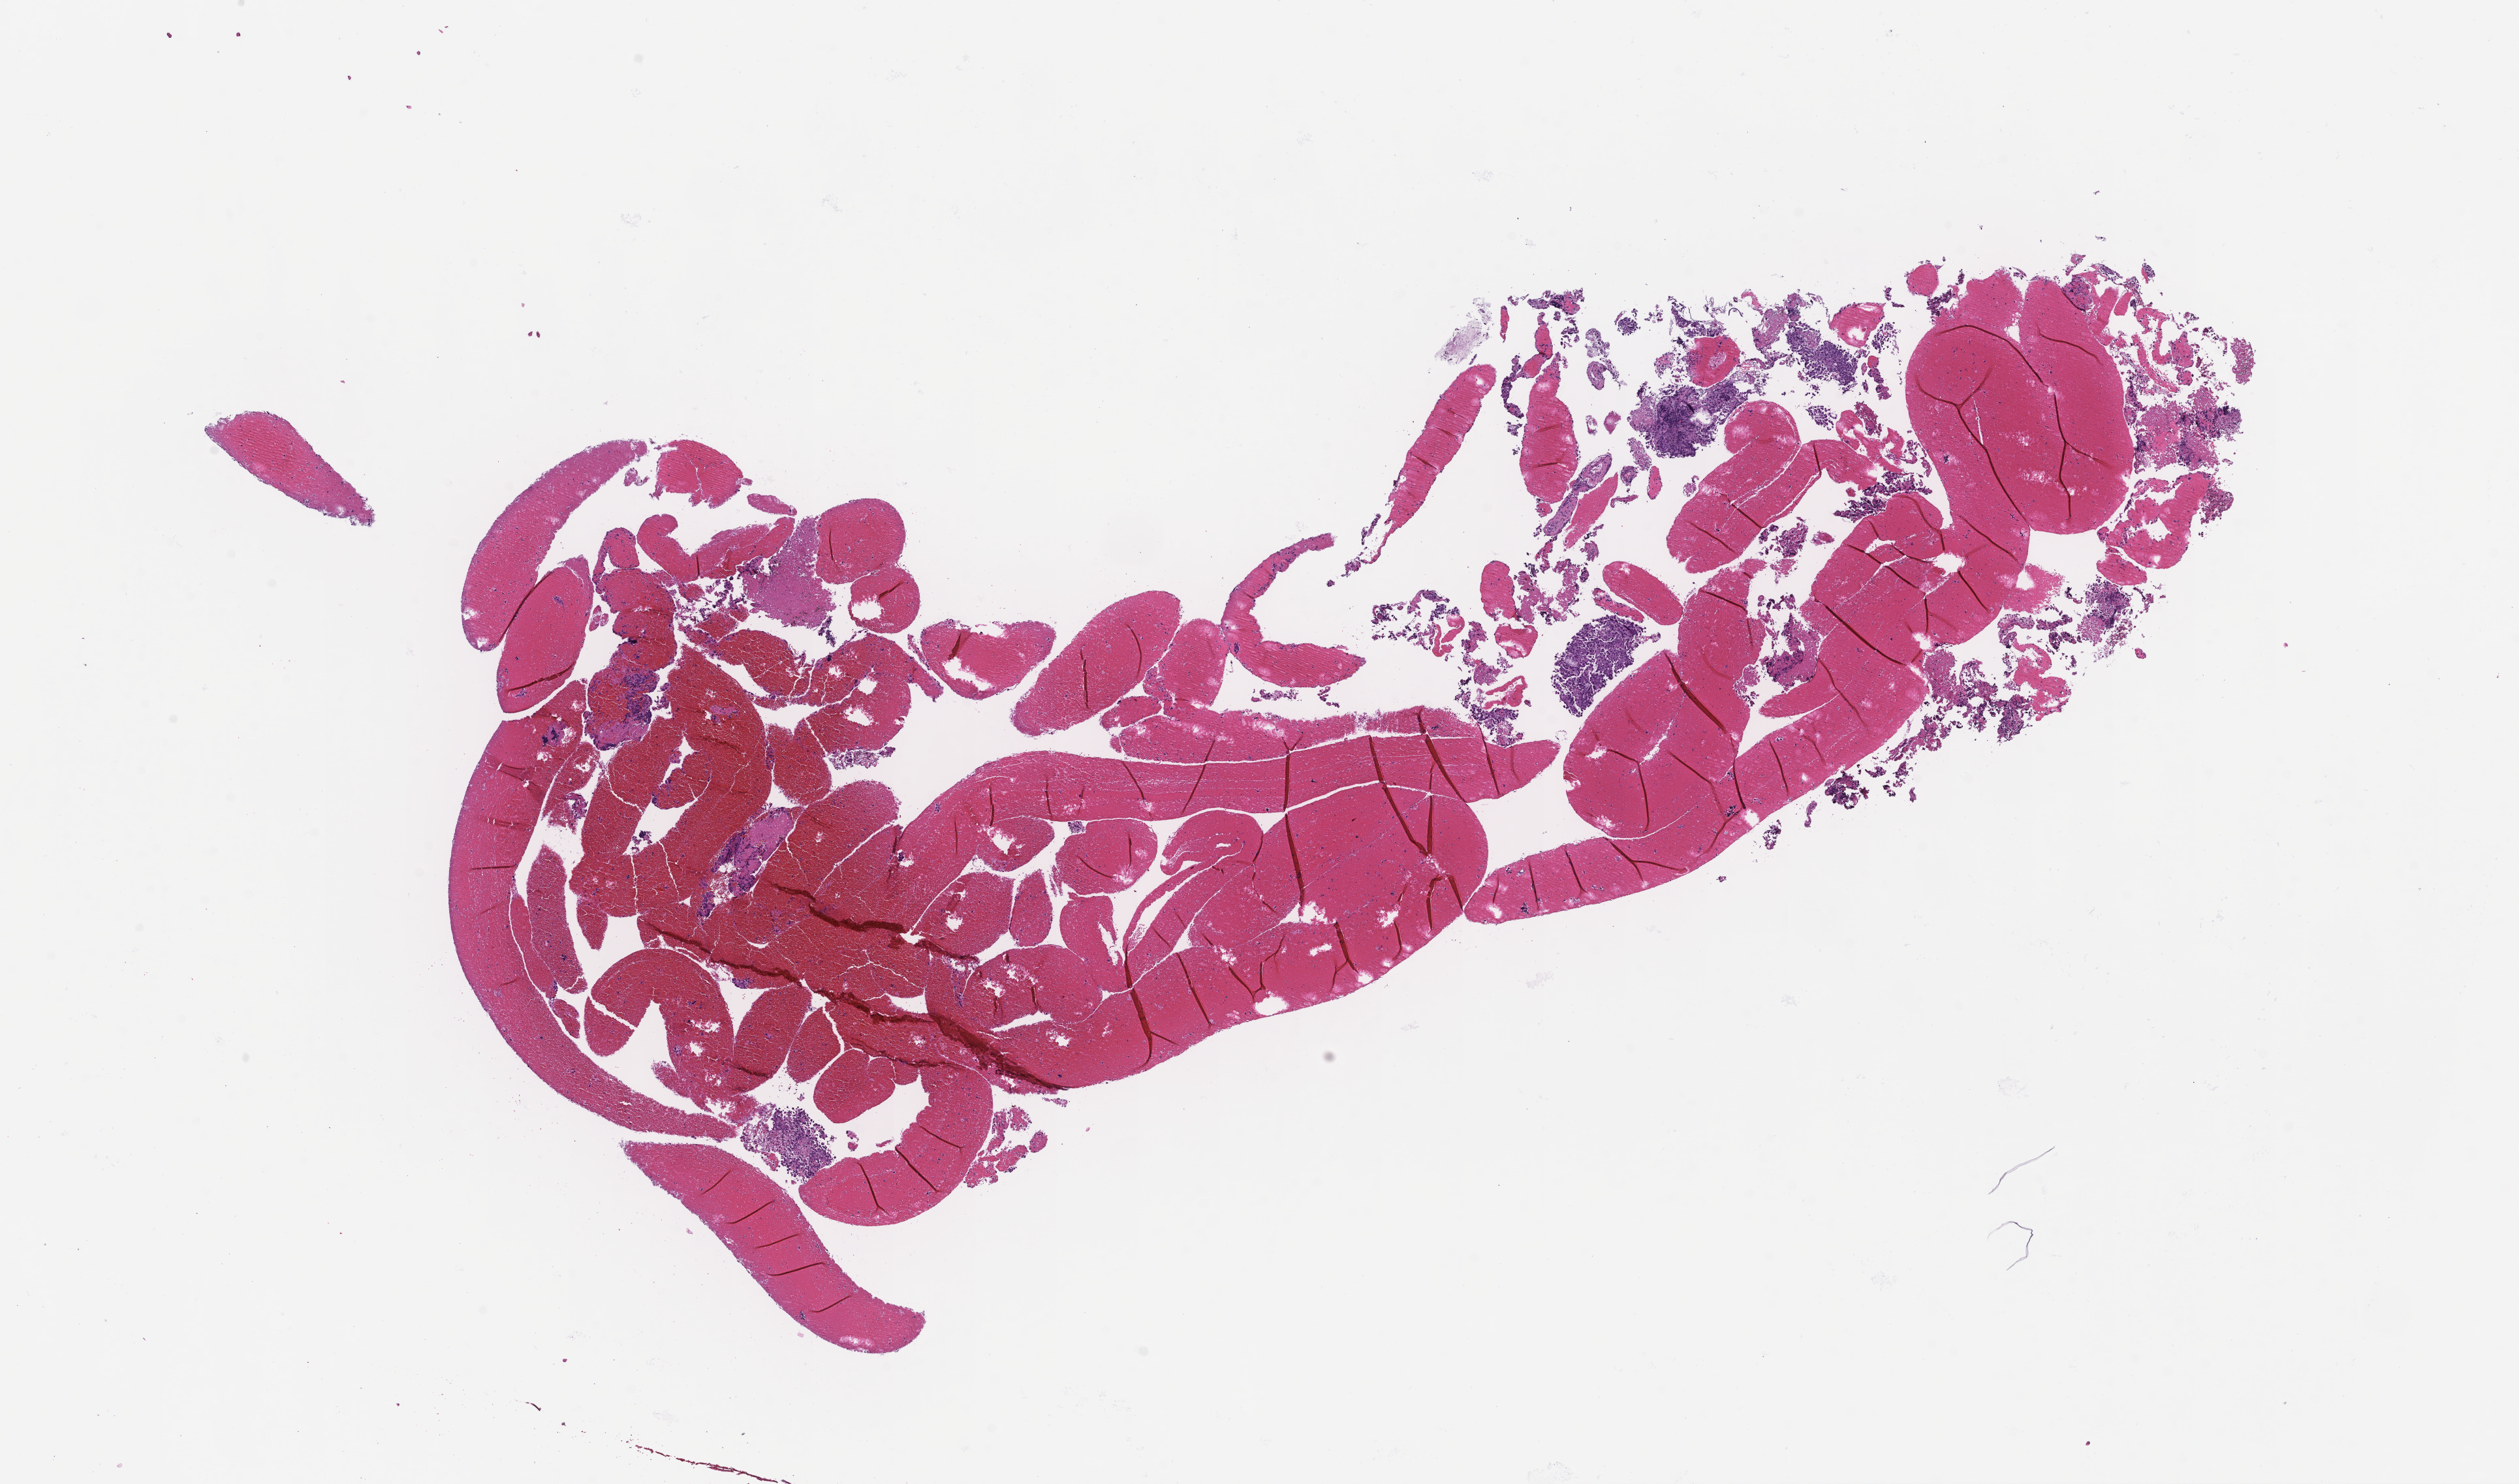
Digitized H&E-stained section — whole scanned area (about 15.6 x 9.2 mm) shown as a low-resolution overview; formalin-fixed, paraffin-embedded (FFPE) tissue; specimen time point: archival tissue. Patient sex: male.
This section: metastatic tumor tissue. Patient diagnosis (primary): Non-Small Cell Lung Carcinoma.